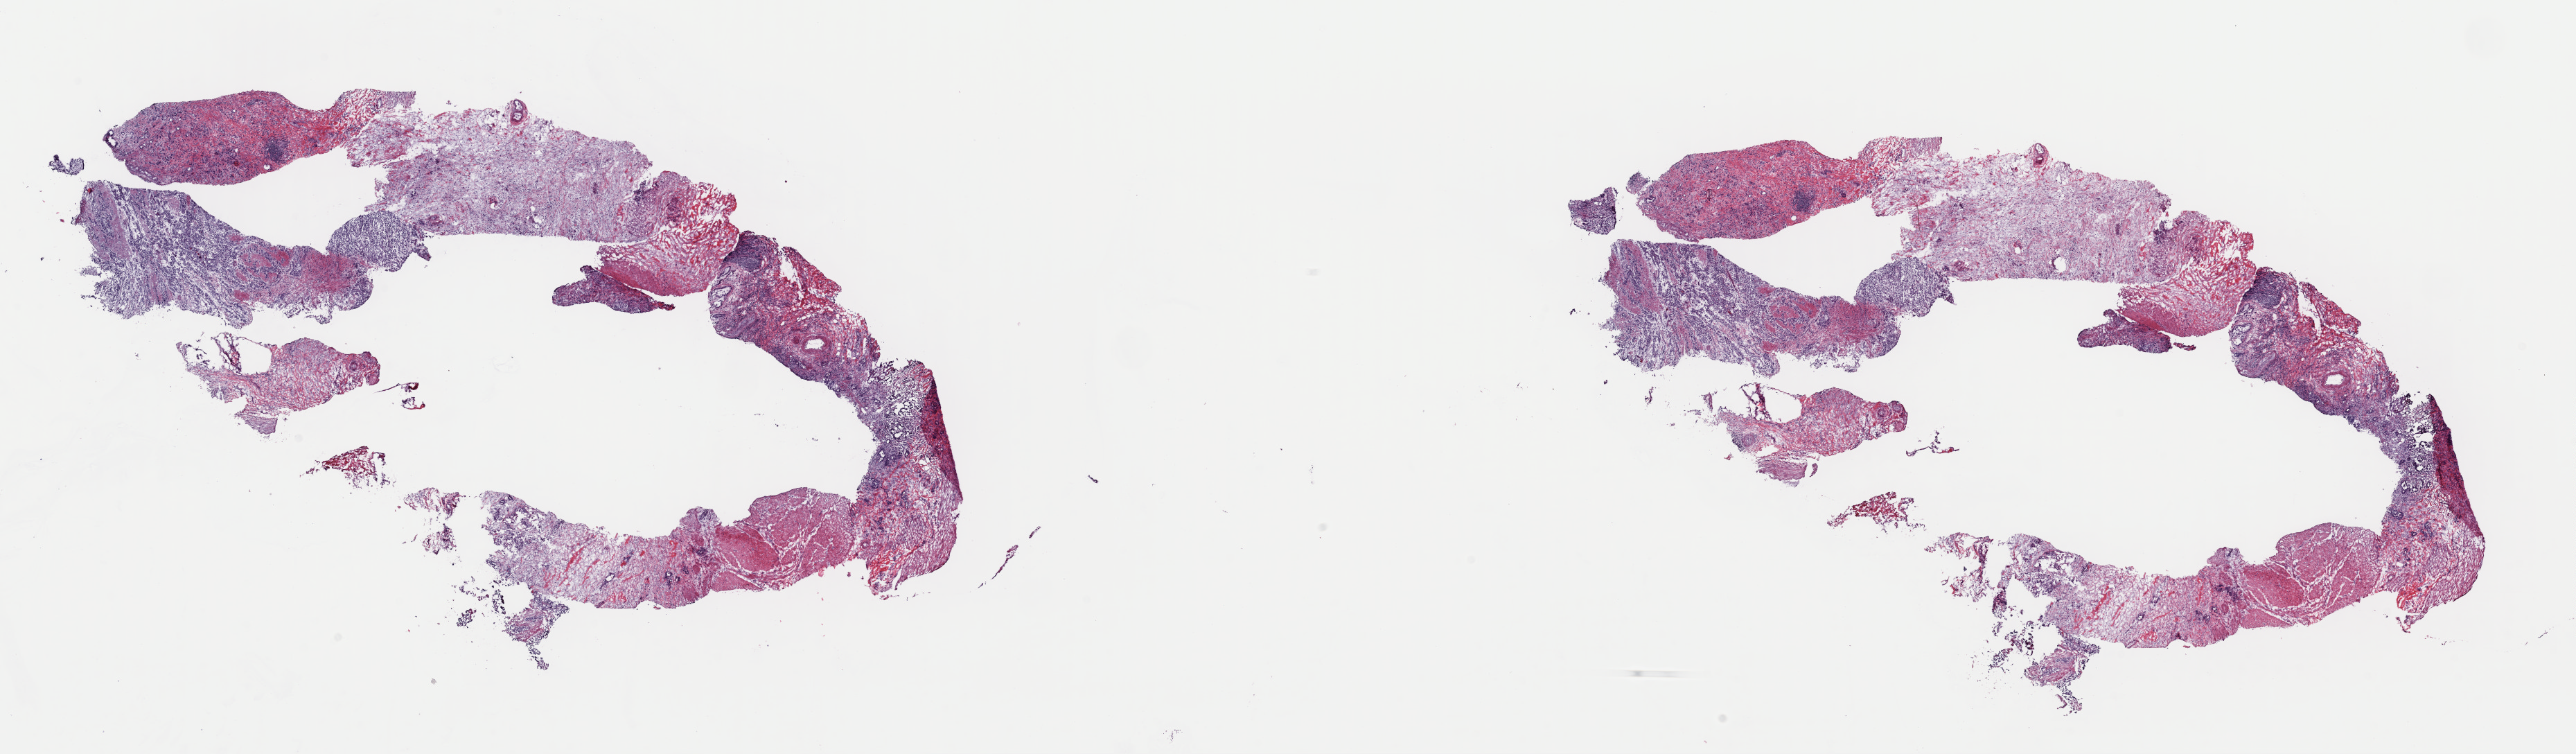
Whole-slide histology image, H&E-stained, low-resolution overview of the scanned area, about 29.4 x 8.6 mm (slide scanned at 40x); frozen section from the top of the tissue portion; primary tumour sample from the stomach. Male patient; age at initial diagnosis 66 years. Histologic grade: G3 (poorly differentiated). Pathologist review of this section (percent, as recorded): tumour cells 80%, tumour nuclei 60%, normal cells 20%, stromal cells 0%, necrosis 0%. Inflammatory infiltration, as recorded: lymphocyte infiltration 5%, monocyte infiltration 0%, neutrophil infiltration 0%.
AJCC pathologic stage: IIA (7th edition). Pathologic diagnosis: Adenocarcinoma, NOS. Lymph nodes positive (case pathology): 0 of 10 examined.